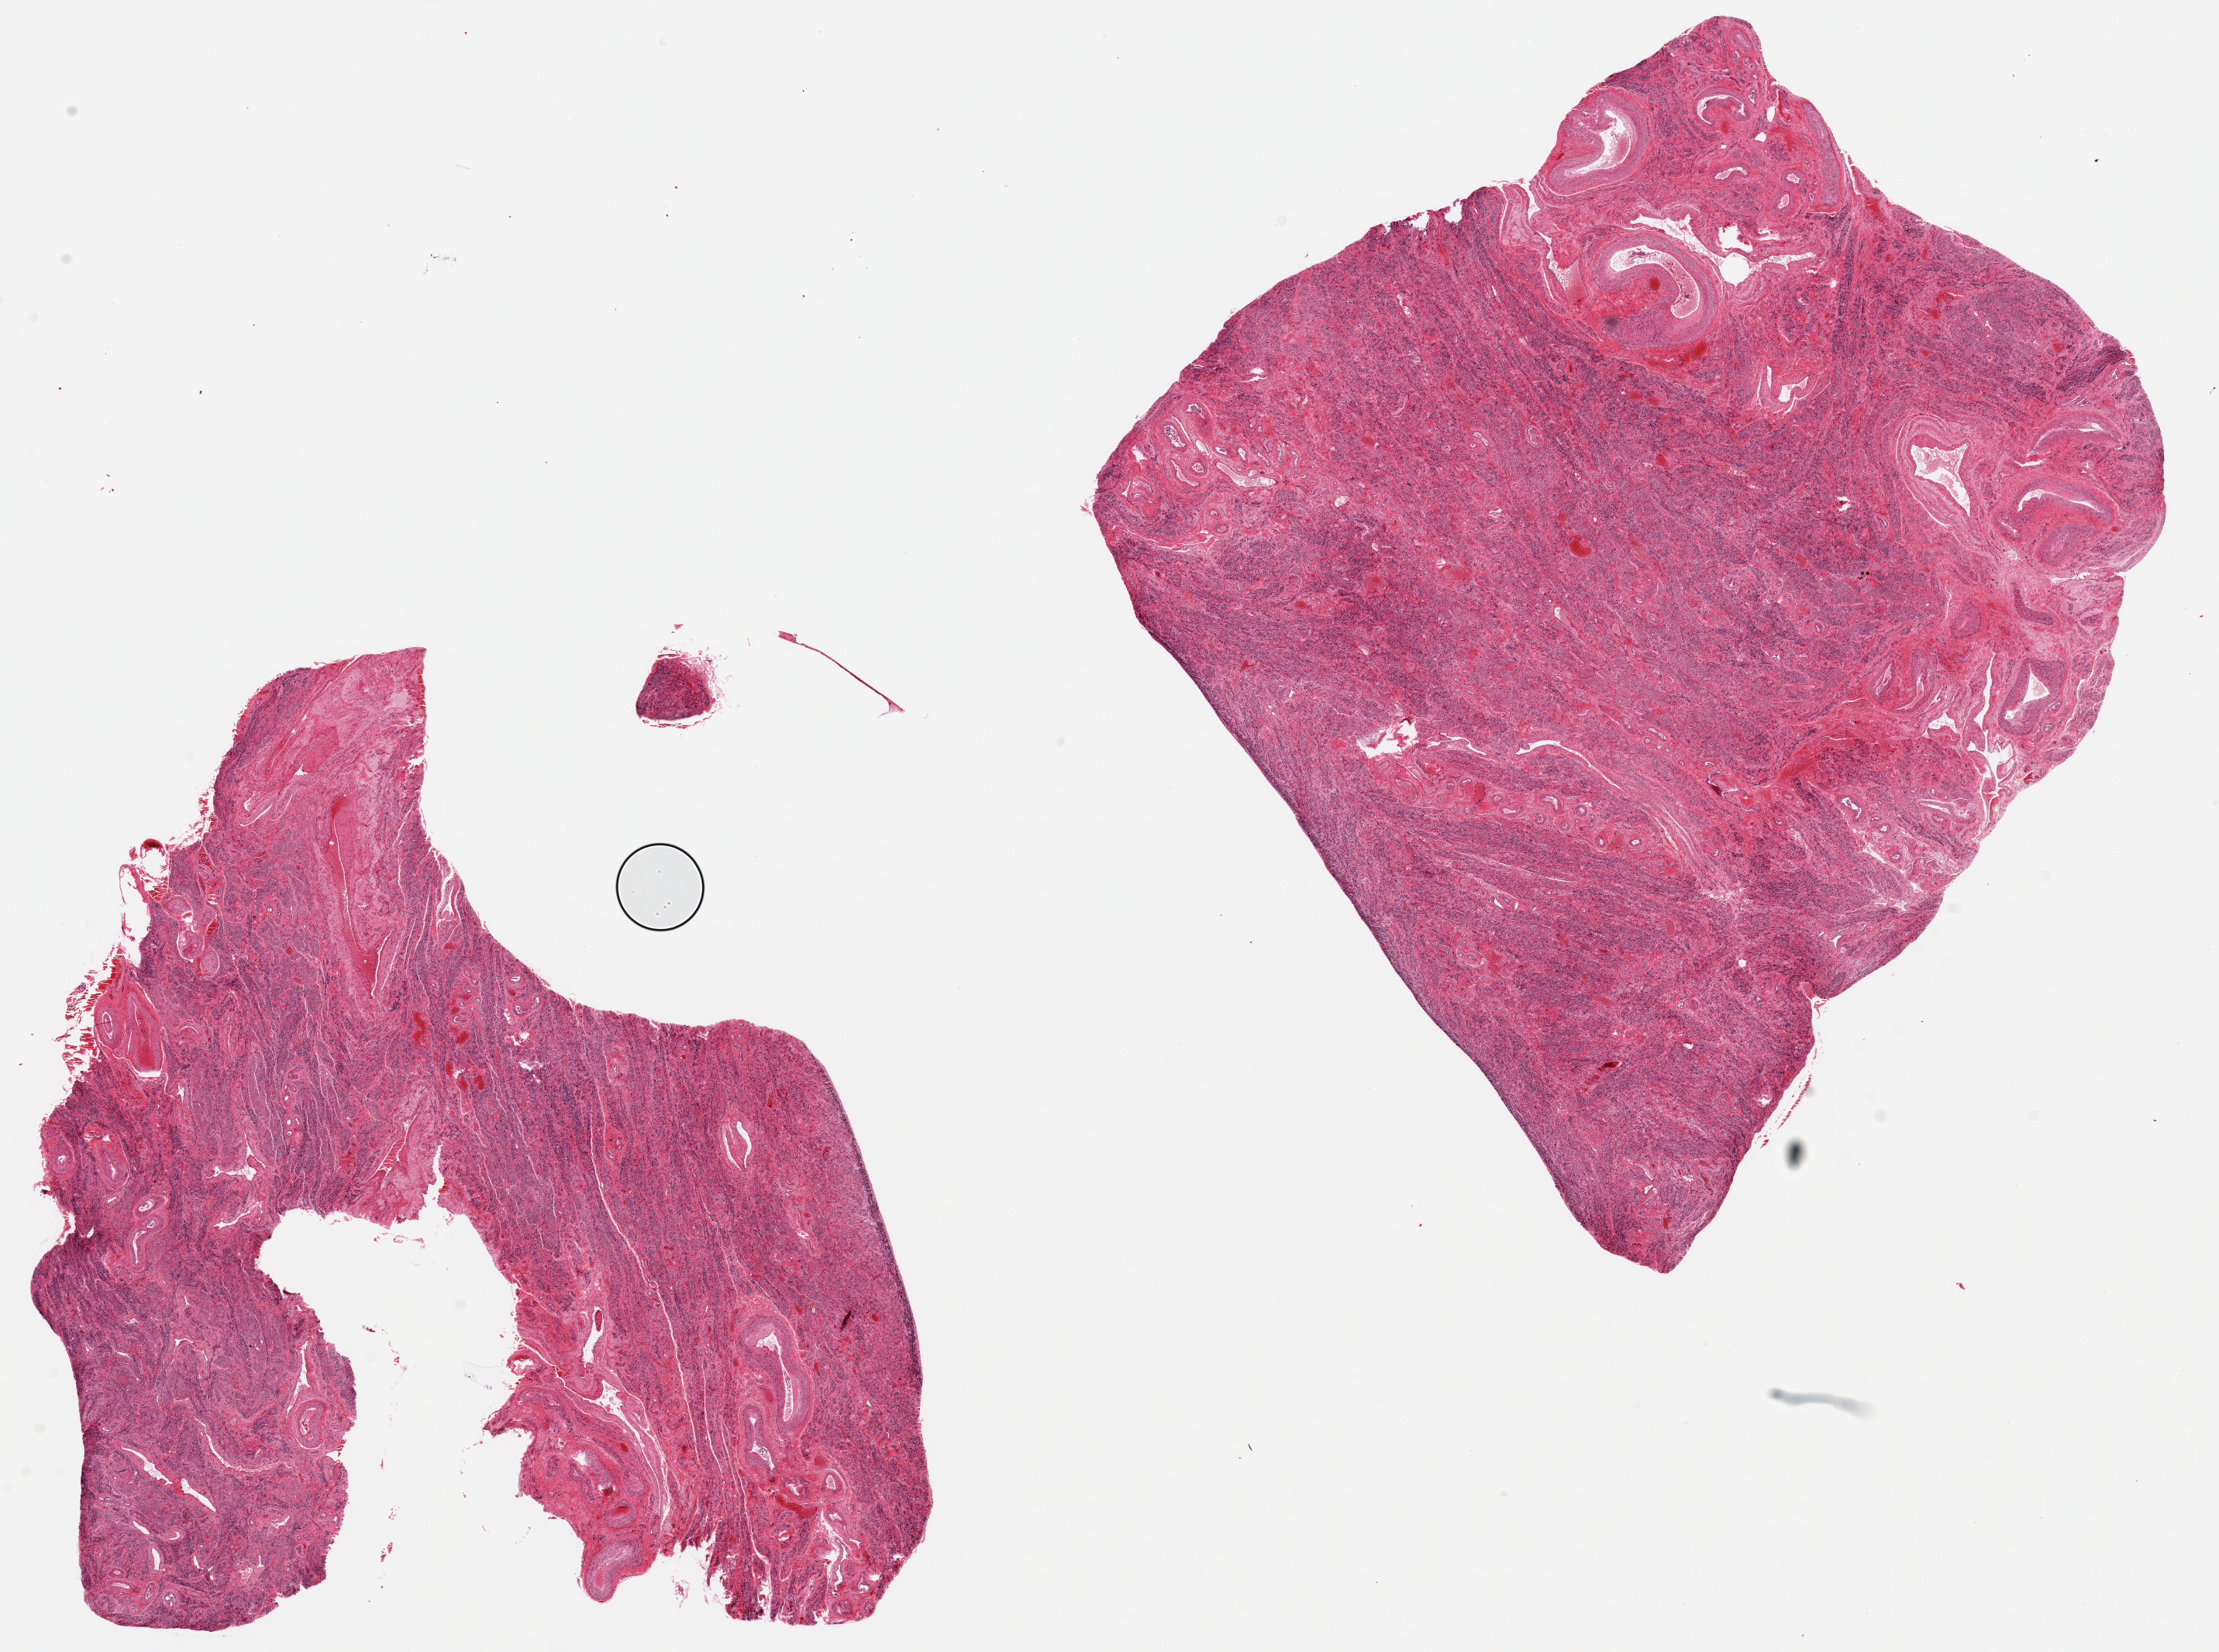
Digitized H&E-stained section, brightfield — low-resolution overview of the scanned area, about 22.6 x 16.9 mm; PAXgene-fixed paraffin-embedded (PFPE) section; sampled site (target tissue): uterus; tissue donor sample. Donor sex: female.
Pathologist's review note for this sample: 2 pieces. 10x9 & 10x9mm; no endometrium, all myometrium.